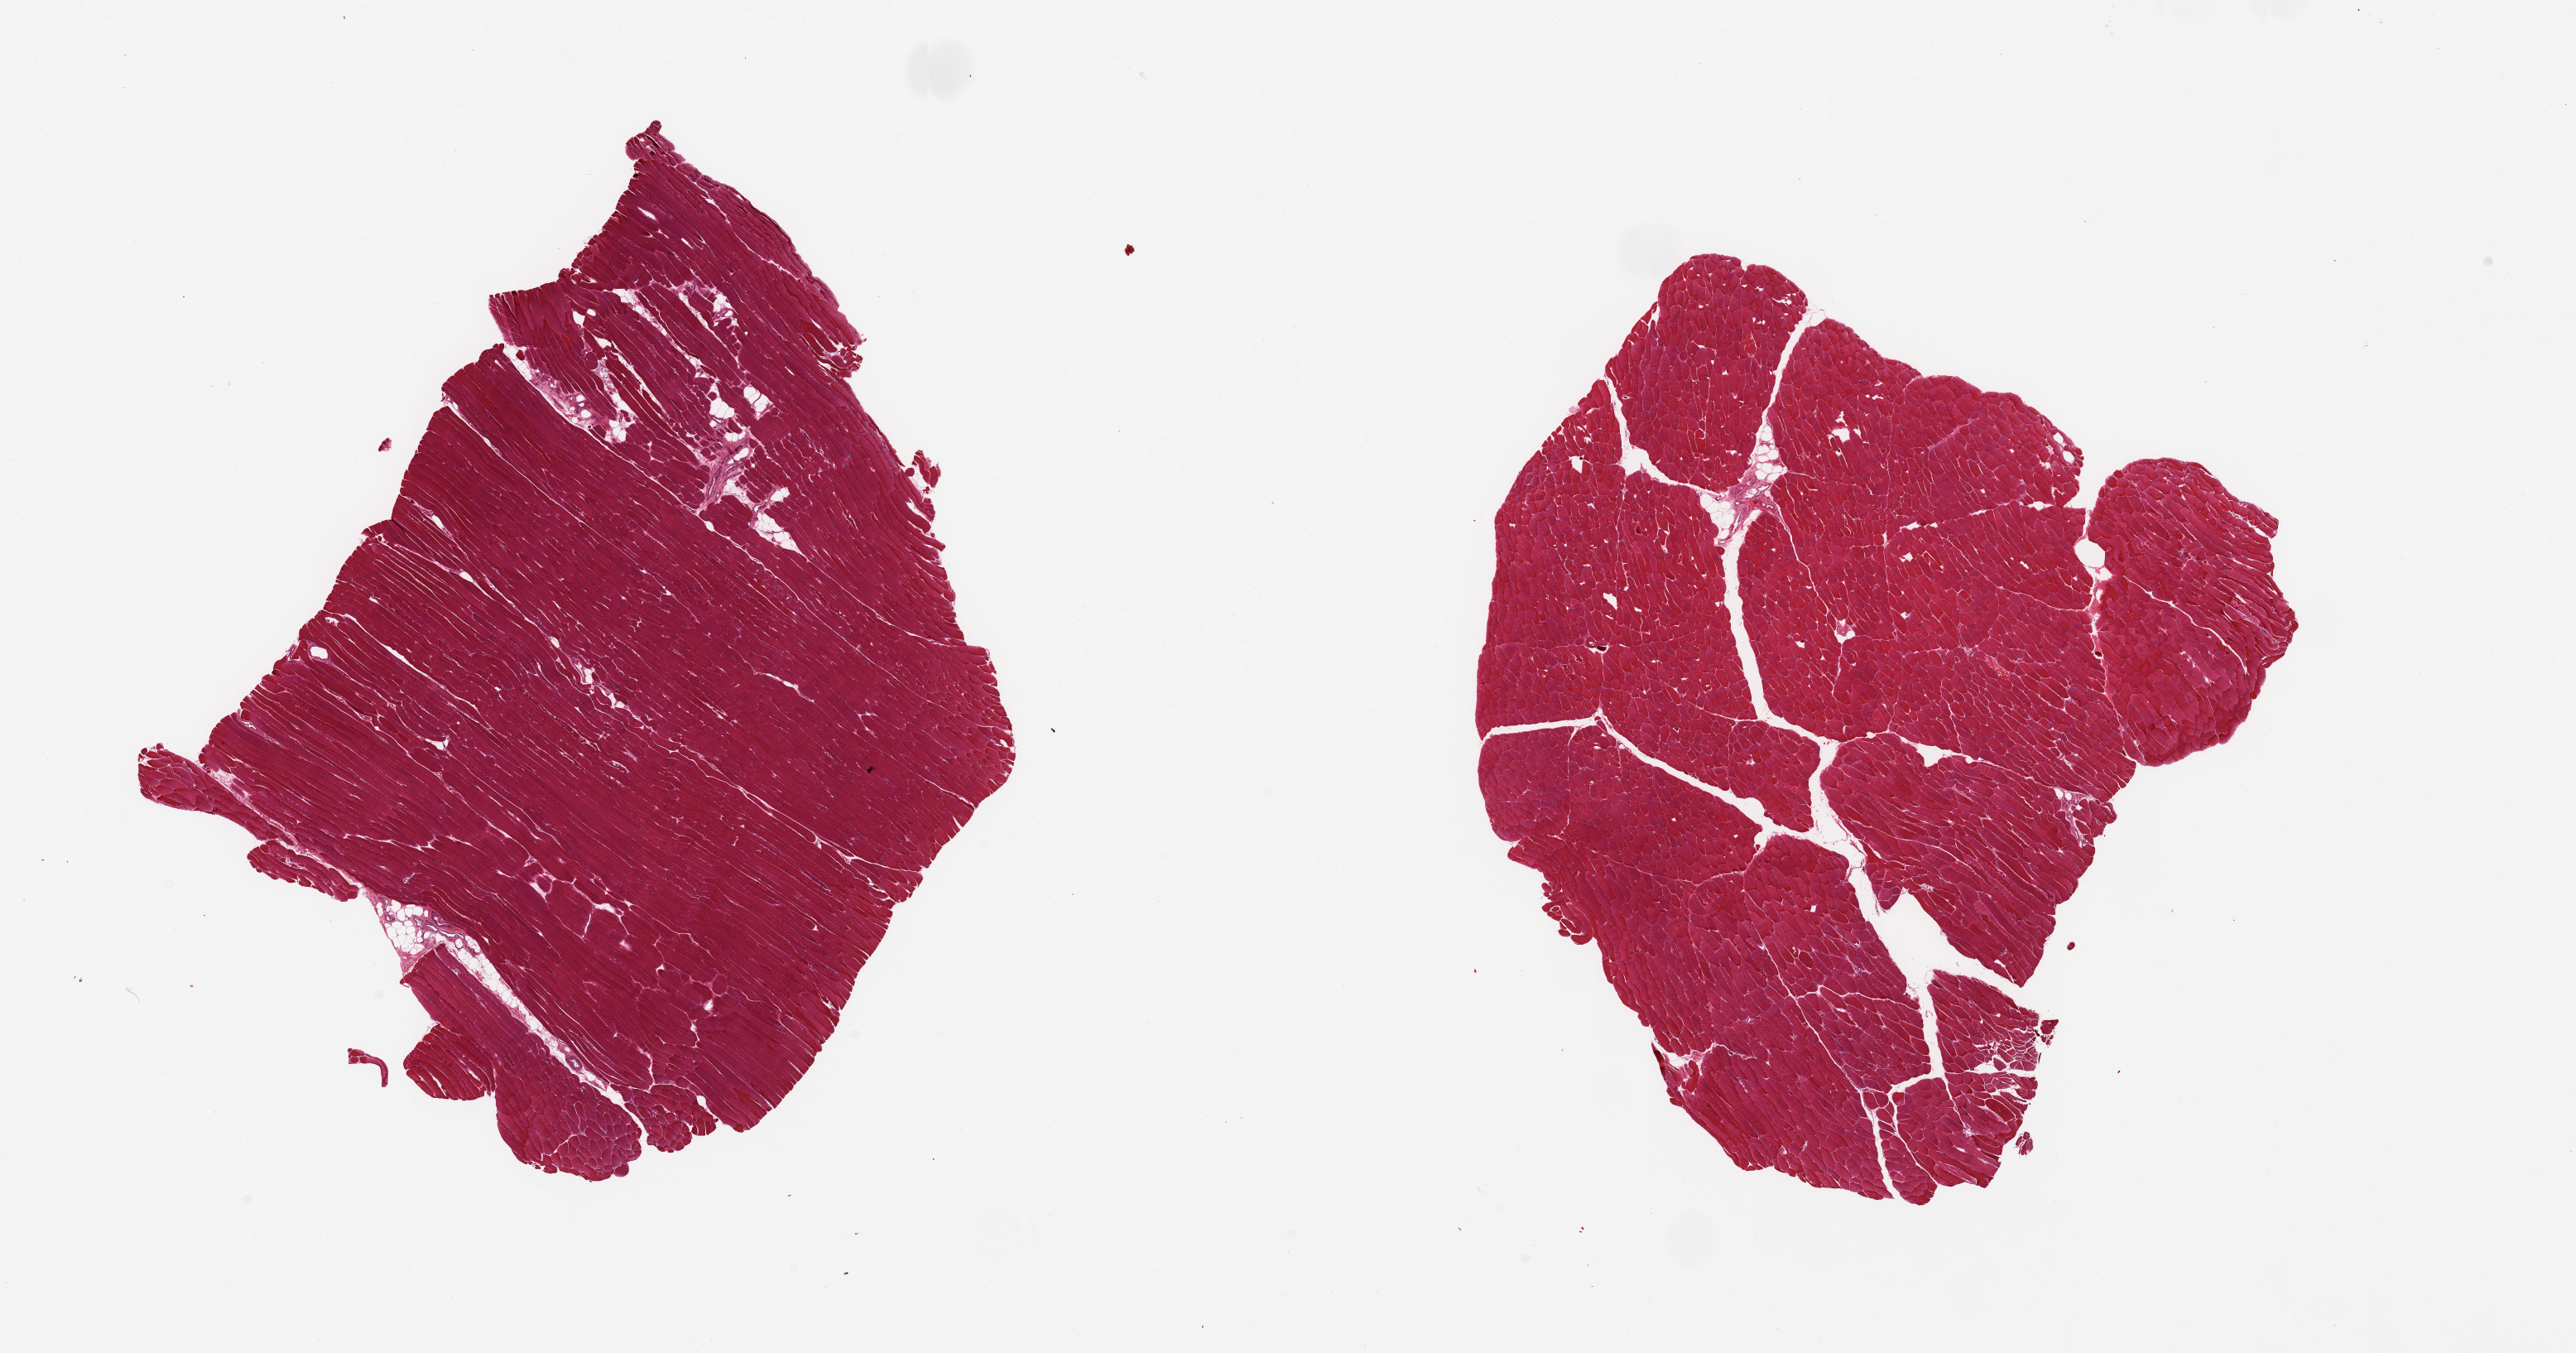
Whole-slide image, H&E stain, whole scanned area (about 24.6 x 12.9 mm) shown as a low-resolution overview; PAXgene-fixed, paraffin-embedded tissue; sampled site (target tissue): skeletal muscle; donor tissue sample. Donor: male.
Review note (as recorded): 2 pieces; scant internal fat.